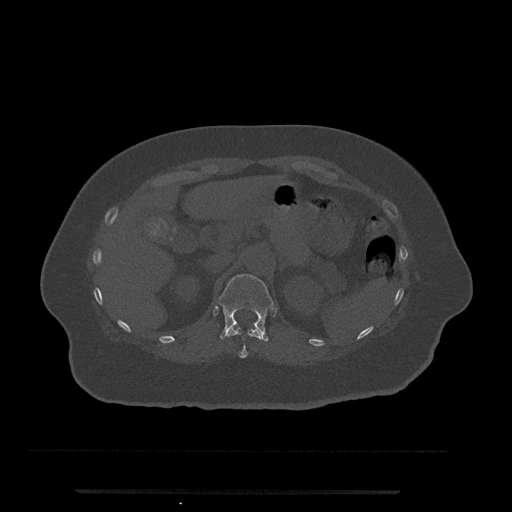
CT including the spine, one axial slice; reconstruction kernel Br40s/3; 120 kVp; bone window (W 1800 / L 400 HU); 0.5 mm slice thickness; 512 × 512 image matrix. Female patient, age 51 years. Case-level facts recorded for this patient, not image findings: primary cancer: neuro; vertebrae with lytic lesions (as recorded): T8.
Structures marked on this image (semi-automatically segmented with operator editing):
- T11 vertebra: bounding box <226,327,261,358> (left, top, right, bottom; pixels)
- T12 vertebra: <218,274,274,342>